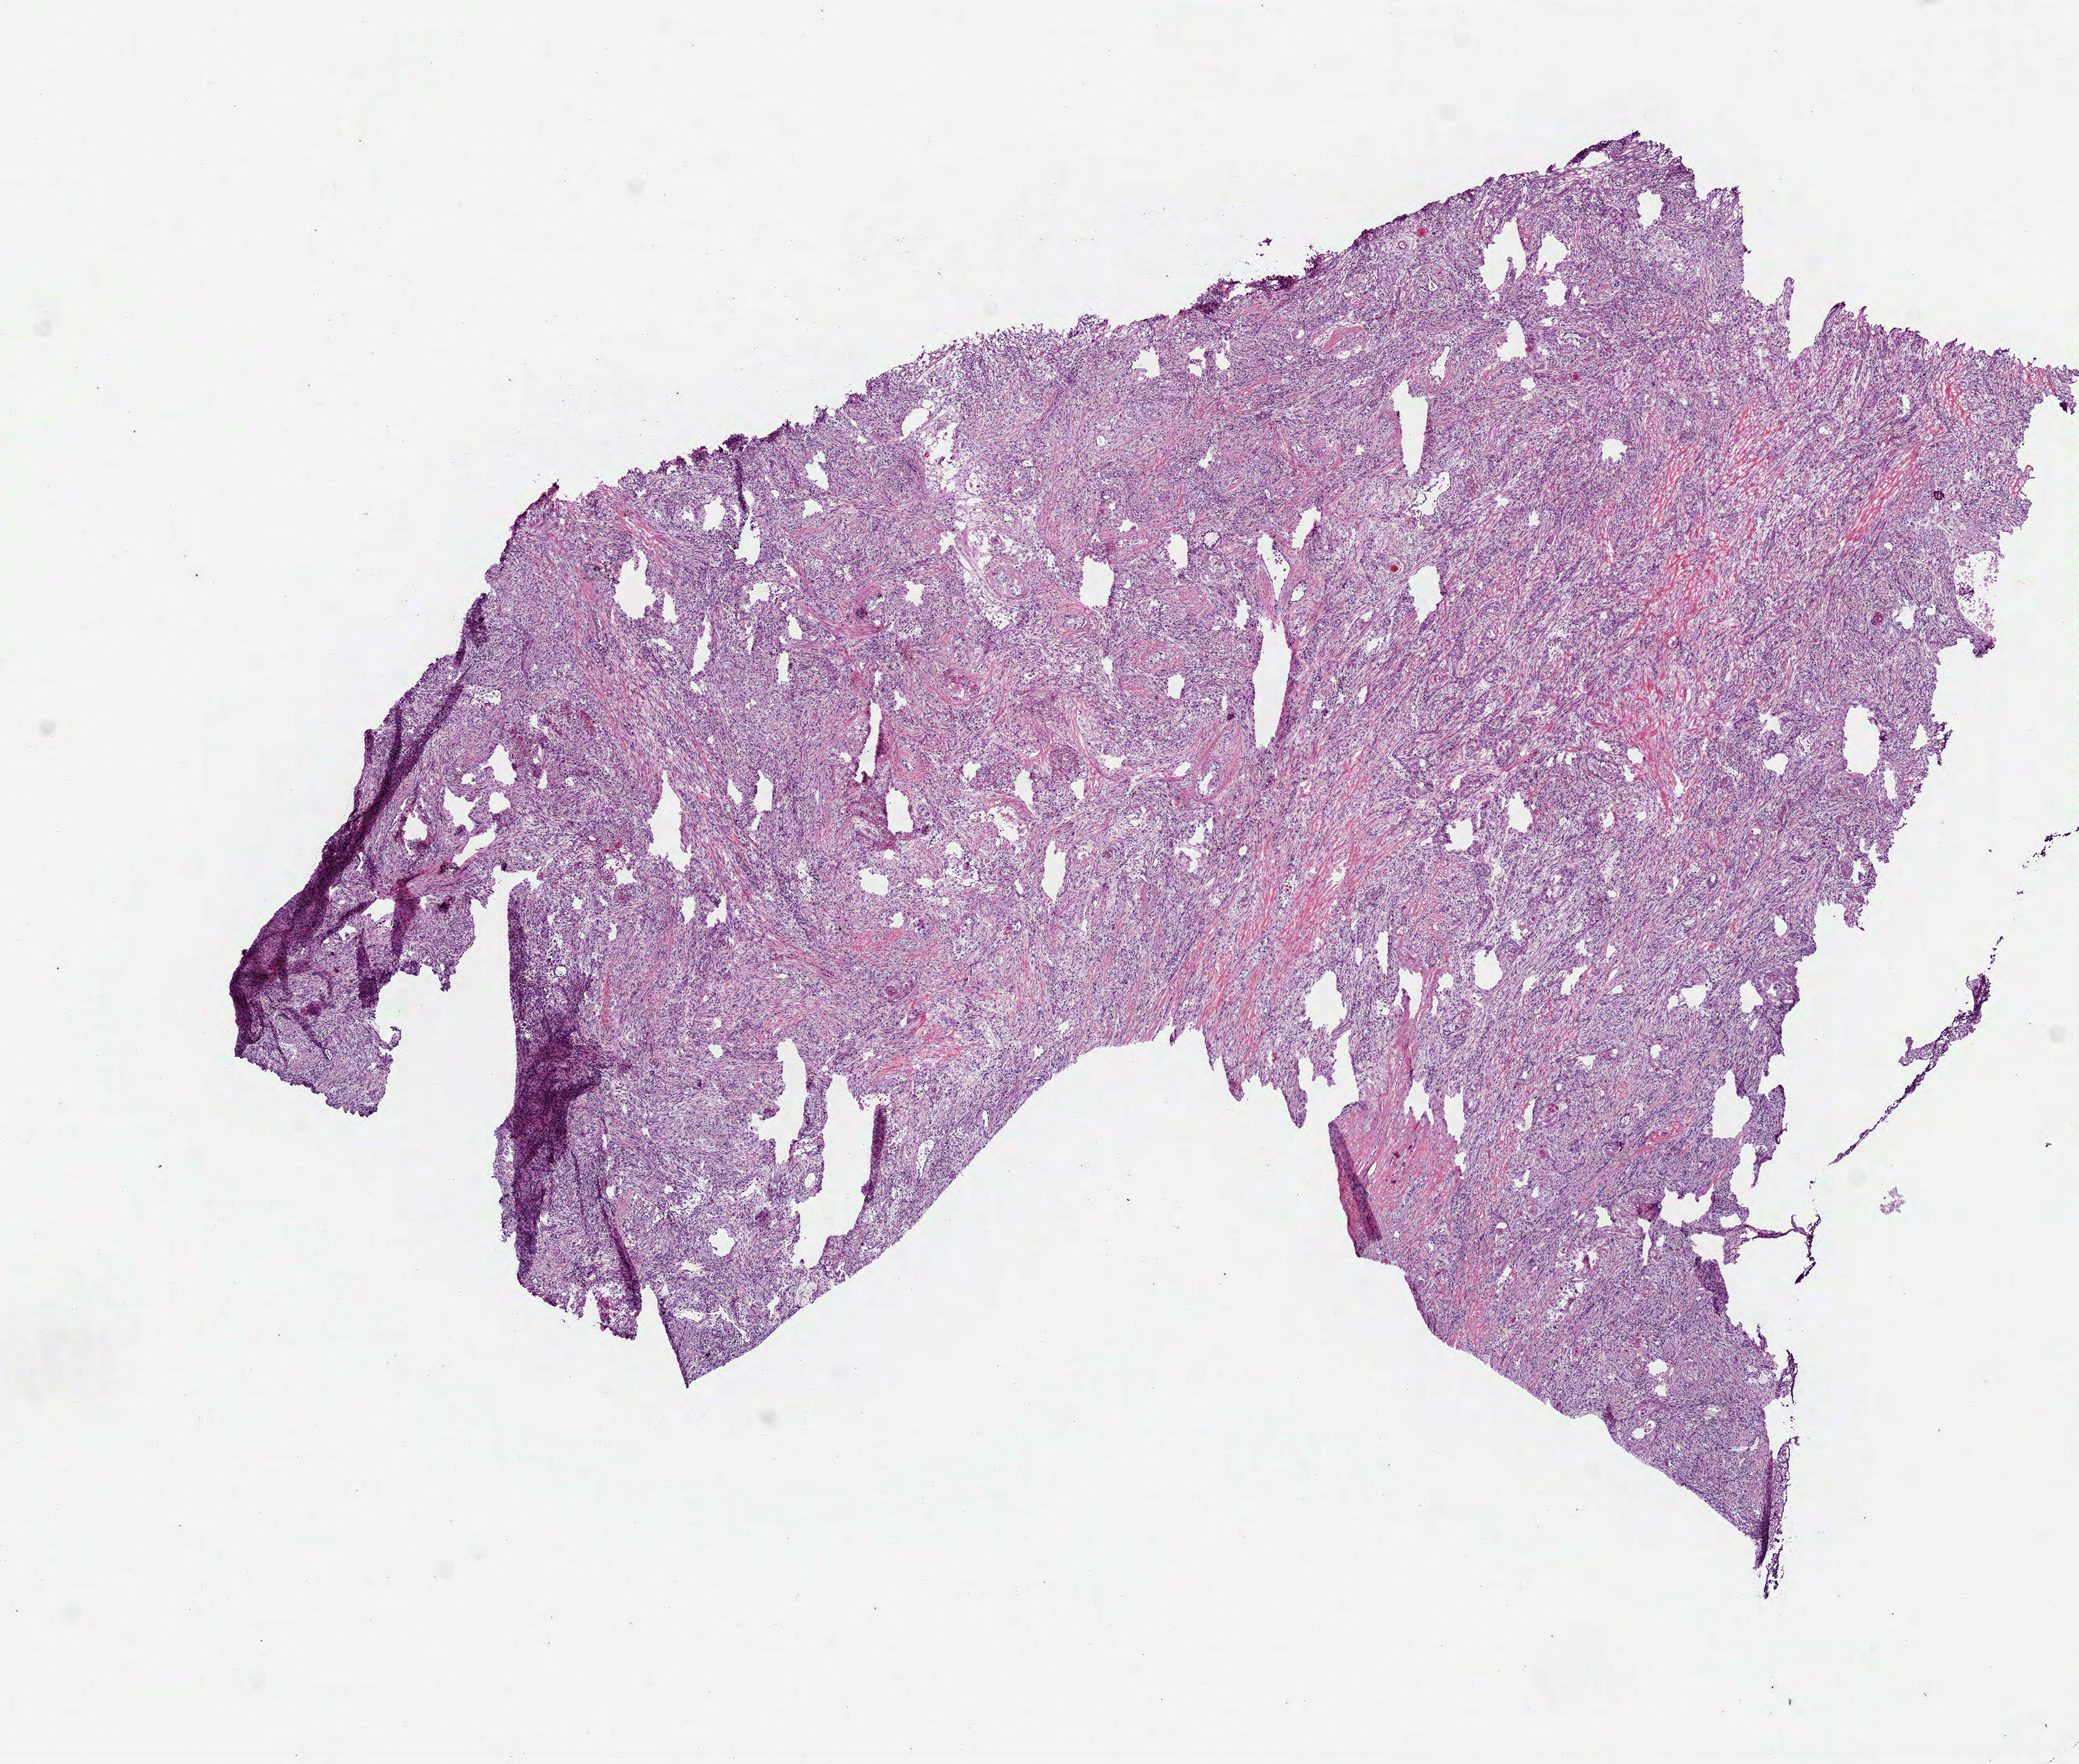
Whole-slide histology image, H&E, whole scanned area (about 10.5 x 8.9 mm, slide scanned at 40x) shown as a low-resolution overview; frozen section; lung, primary tumour sample. Male patient; age at initial diagnosis 68 years.
Histologic diagnosis: Squamous cell carcinoma, keratinizing, NOS (lower lobe, lung).